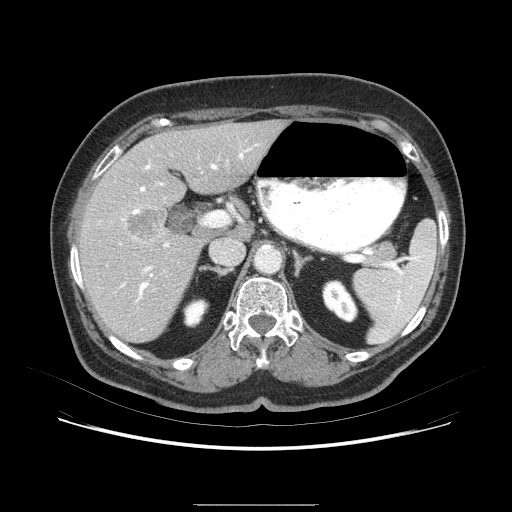
Contrast-enhanced abdominal CT (liver protocol), one axial slice. Position 45 of 79 along the scan axis. 120 kVp. Soft-tissue window (W 400 / L 40 HU). 2.5 mm slice thickness. 512 × 512 image matrix, field of view 380 × 380 mm. Case-level facts recorded for this patient, not image findings: diagnosis: hepatocellular carcinoma (patient treated with transarterial chemoembolisation; whether this scan precedes or follows treatment is not stated here); TNM stage (as recorded): Stage-I; Child-Pugh class: A; tumour differentiation: poorly differentiated.
Structures marked on this image (semi-automatic segmentation, software-assisted and operator-edited):
- liver parenchyma outside the tumour (the mass and vessels are separate outlines, so this box may not span the whole liver): bounding box [x1, y1, x2, y2] px = [78, 122, 293, 346]
- mass: [126, 202, 173, 239]
- liver vessels: [84, 140, 274, 320]